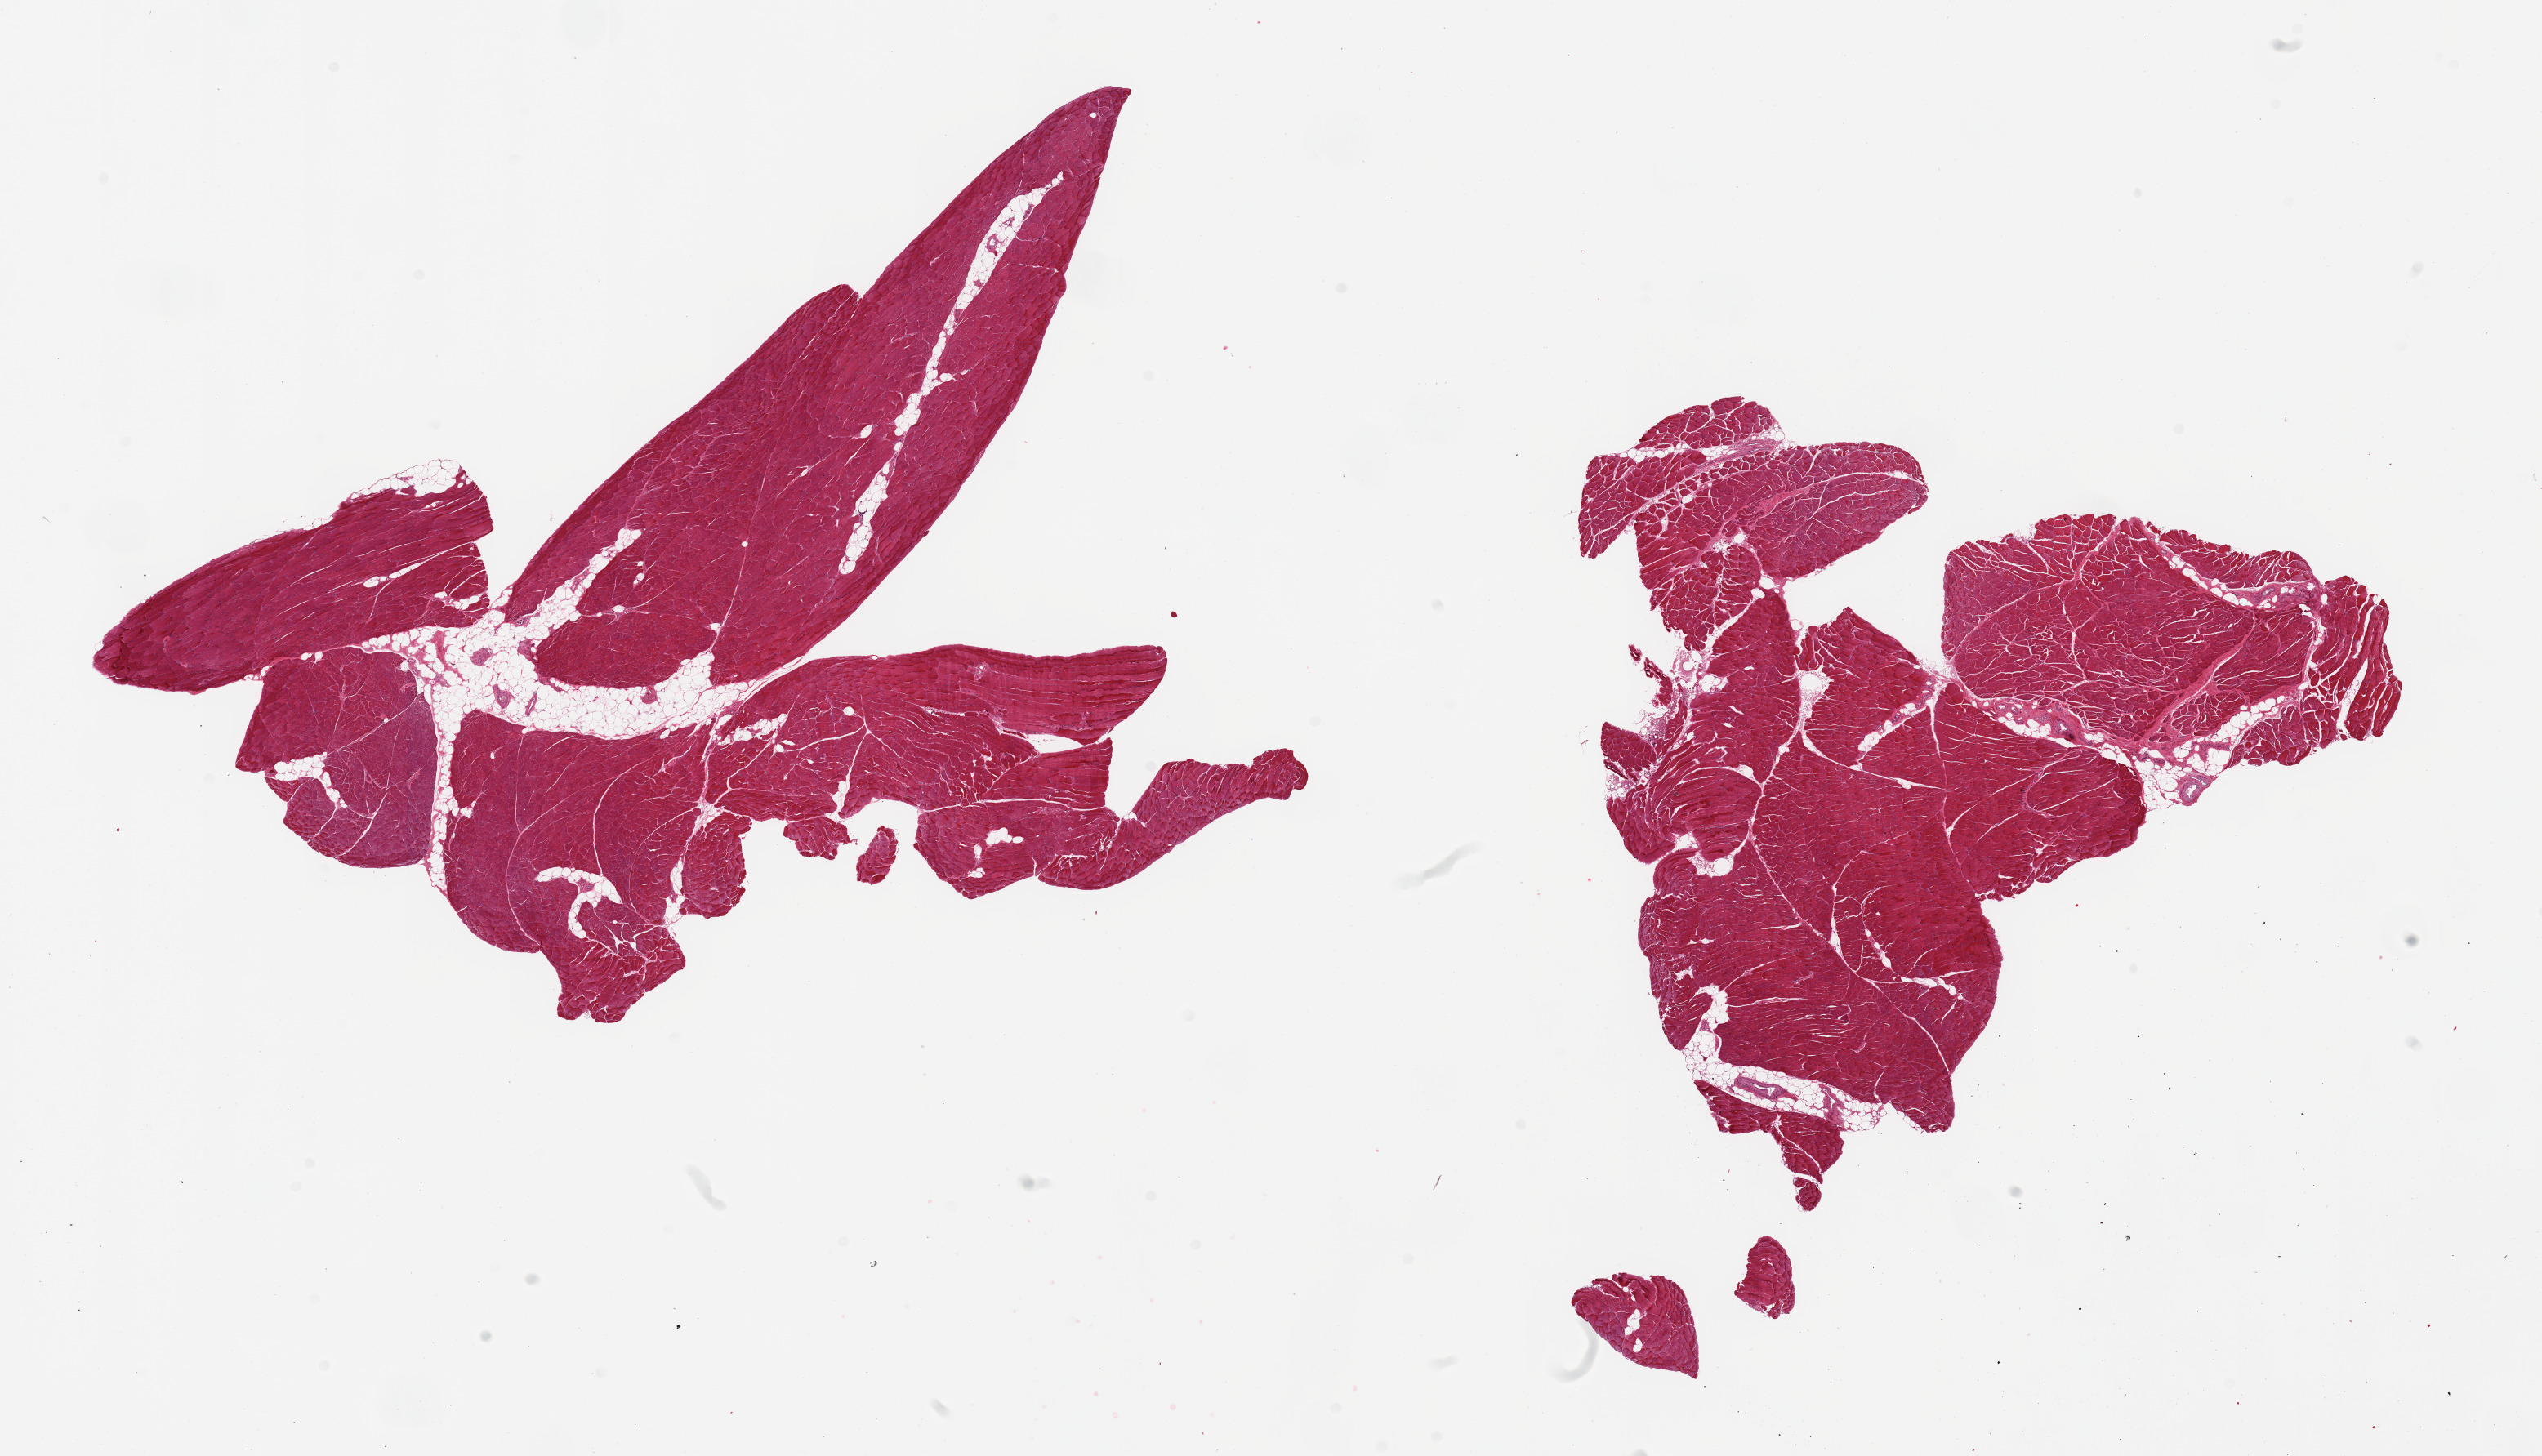
Digitized hematoxylin and eosin (H&E)-stained section, a low-resolution overview of the entire scanned area, about 24.6 x 14.1 mm (from a 20x scan), PAXgene-fixed paraffin-embedded (PFPE) section, target tissue: skeletal muscle, tissue donor sample. Donor sex: female.
- pathologist's review note for this sample: 2 pieces; up to 10% internal fat